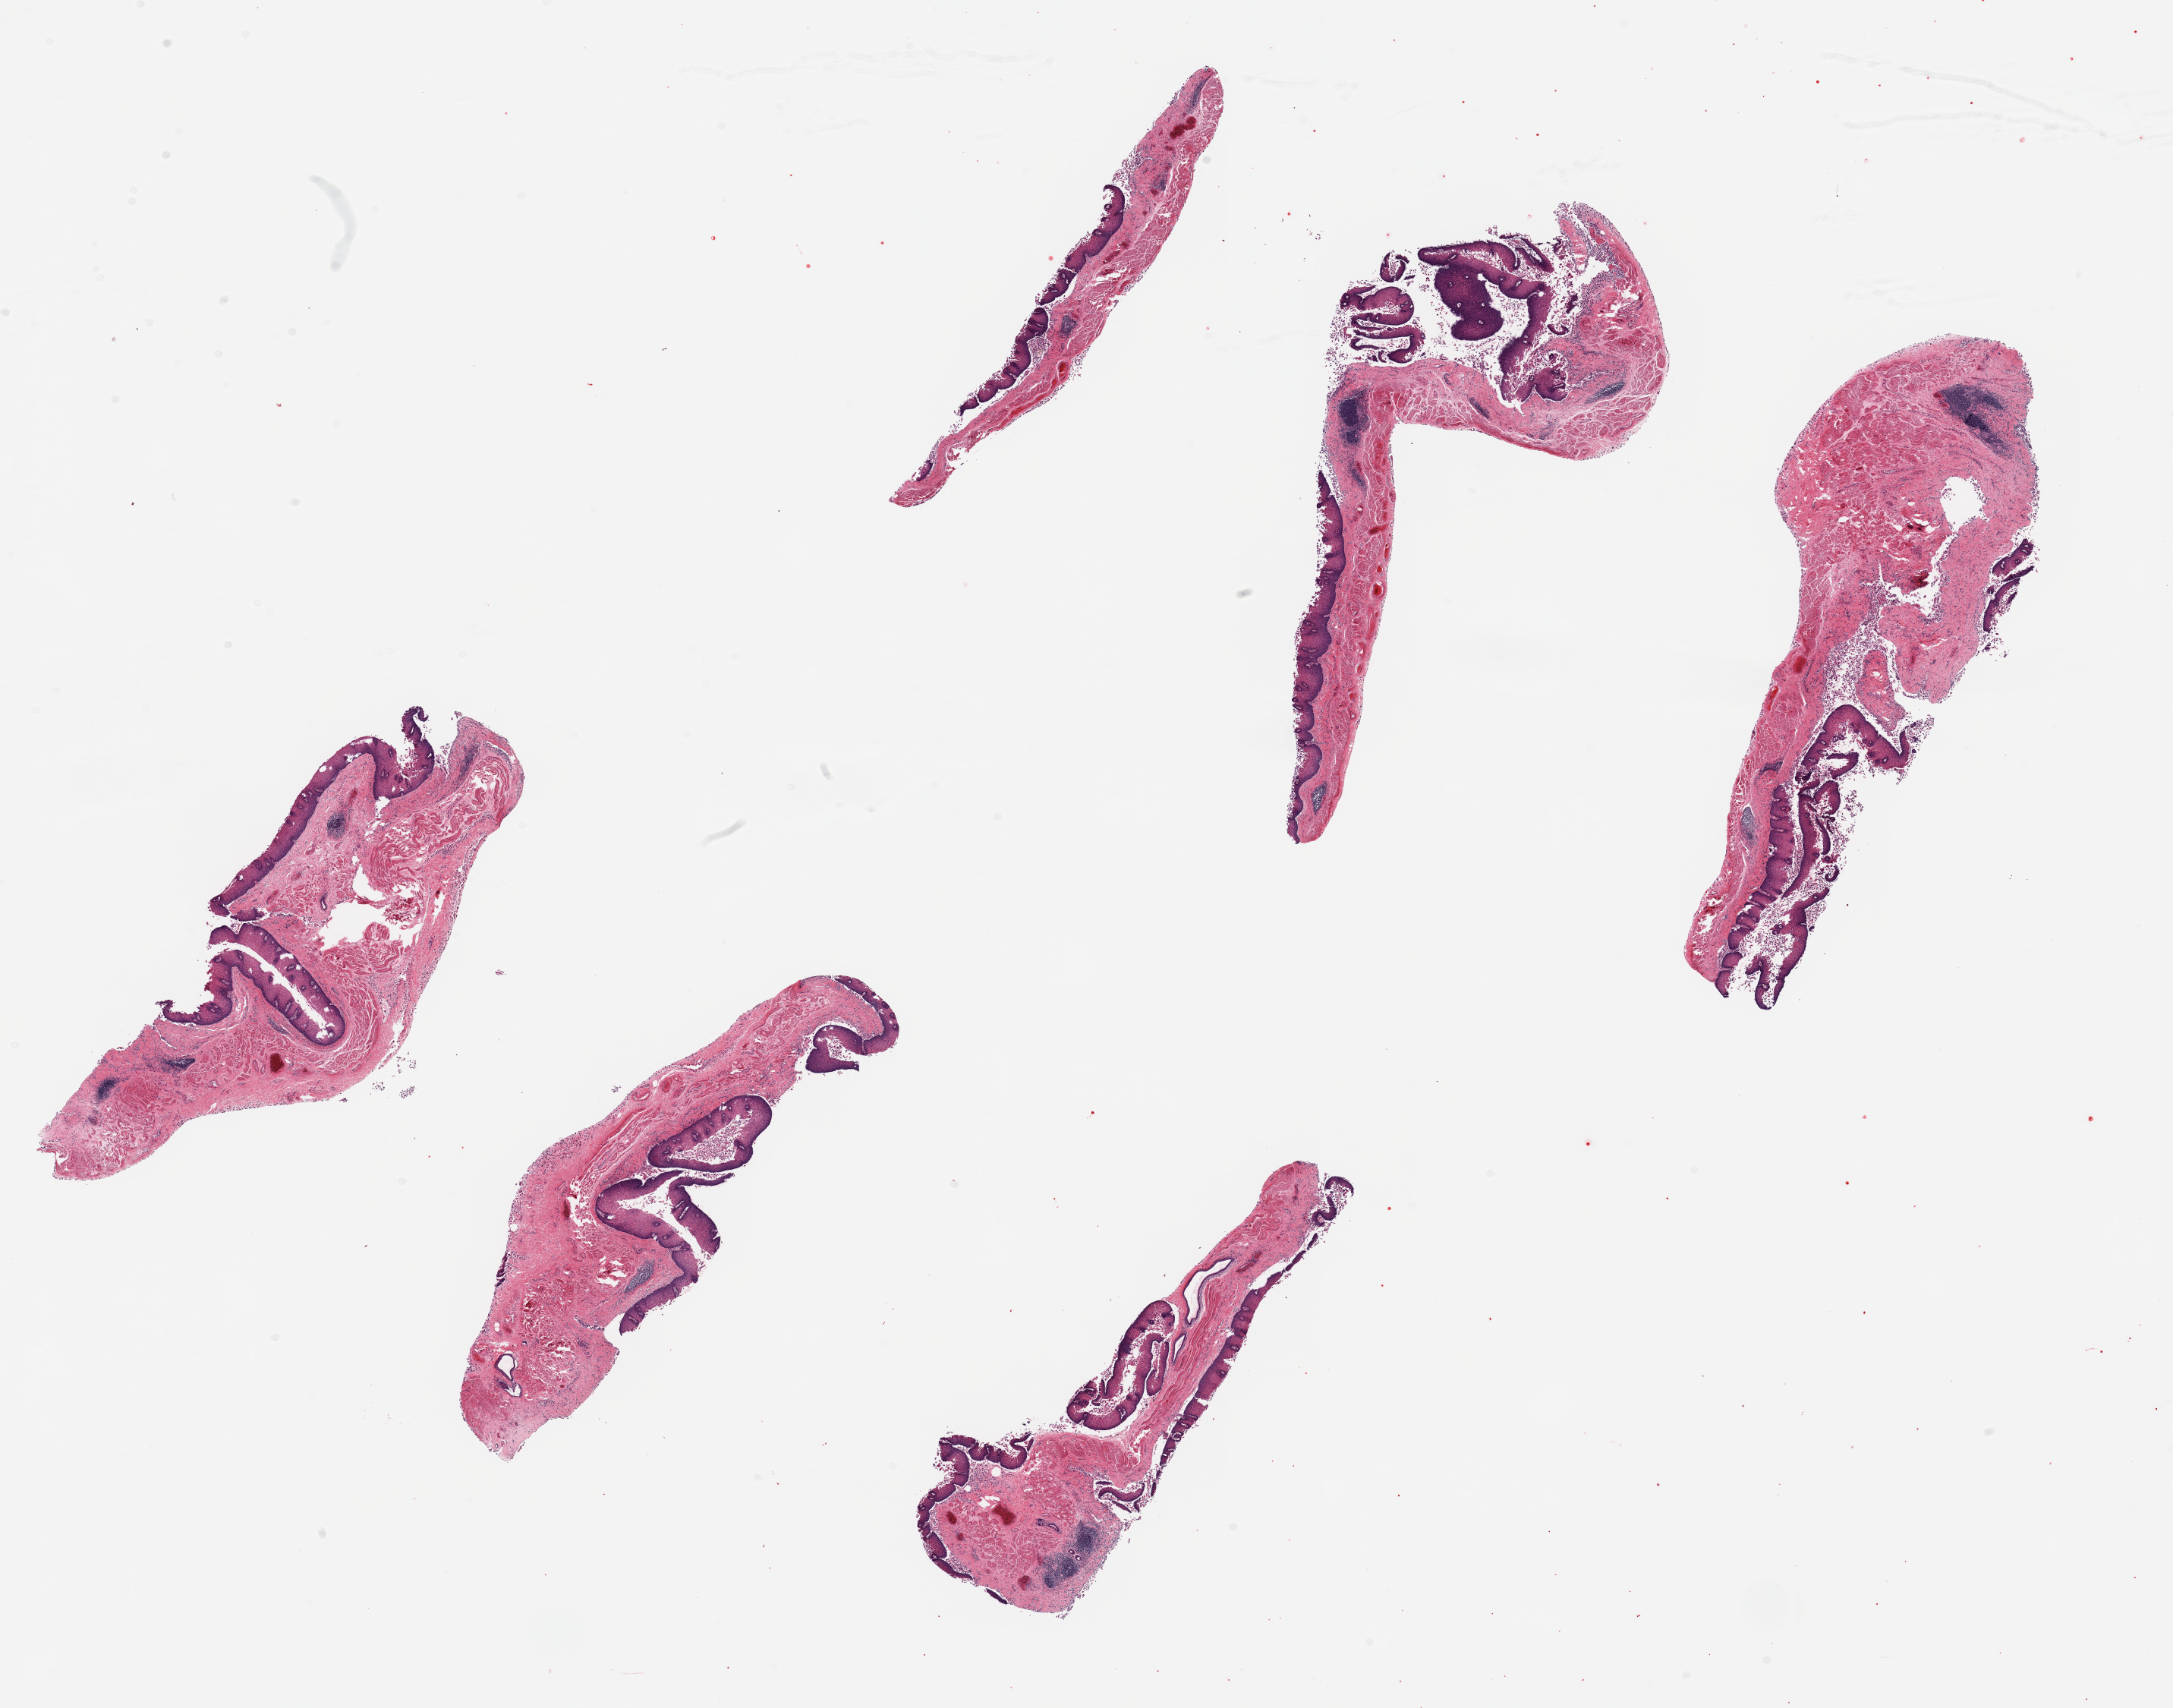
Digitized haematoxylin and eosin-stained section, brightfield, whole scanned area (about 22.6 x 17.8 mm) shown as a low-resolution overview; PAXgene-fixed paraffin-embedded (PFPE) section; sampled site (target tissue): esophageal mucous membrane; tissue donor sample. Male donor.
Pathologist's review note for this sample: 6 ~6x1.5mm pieces. Squamous mucosa is ~10-15% of thickness.